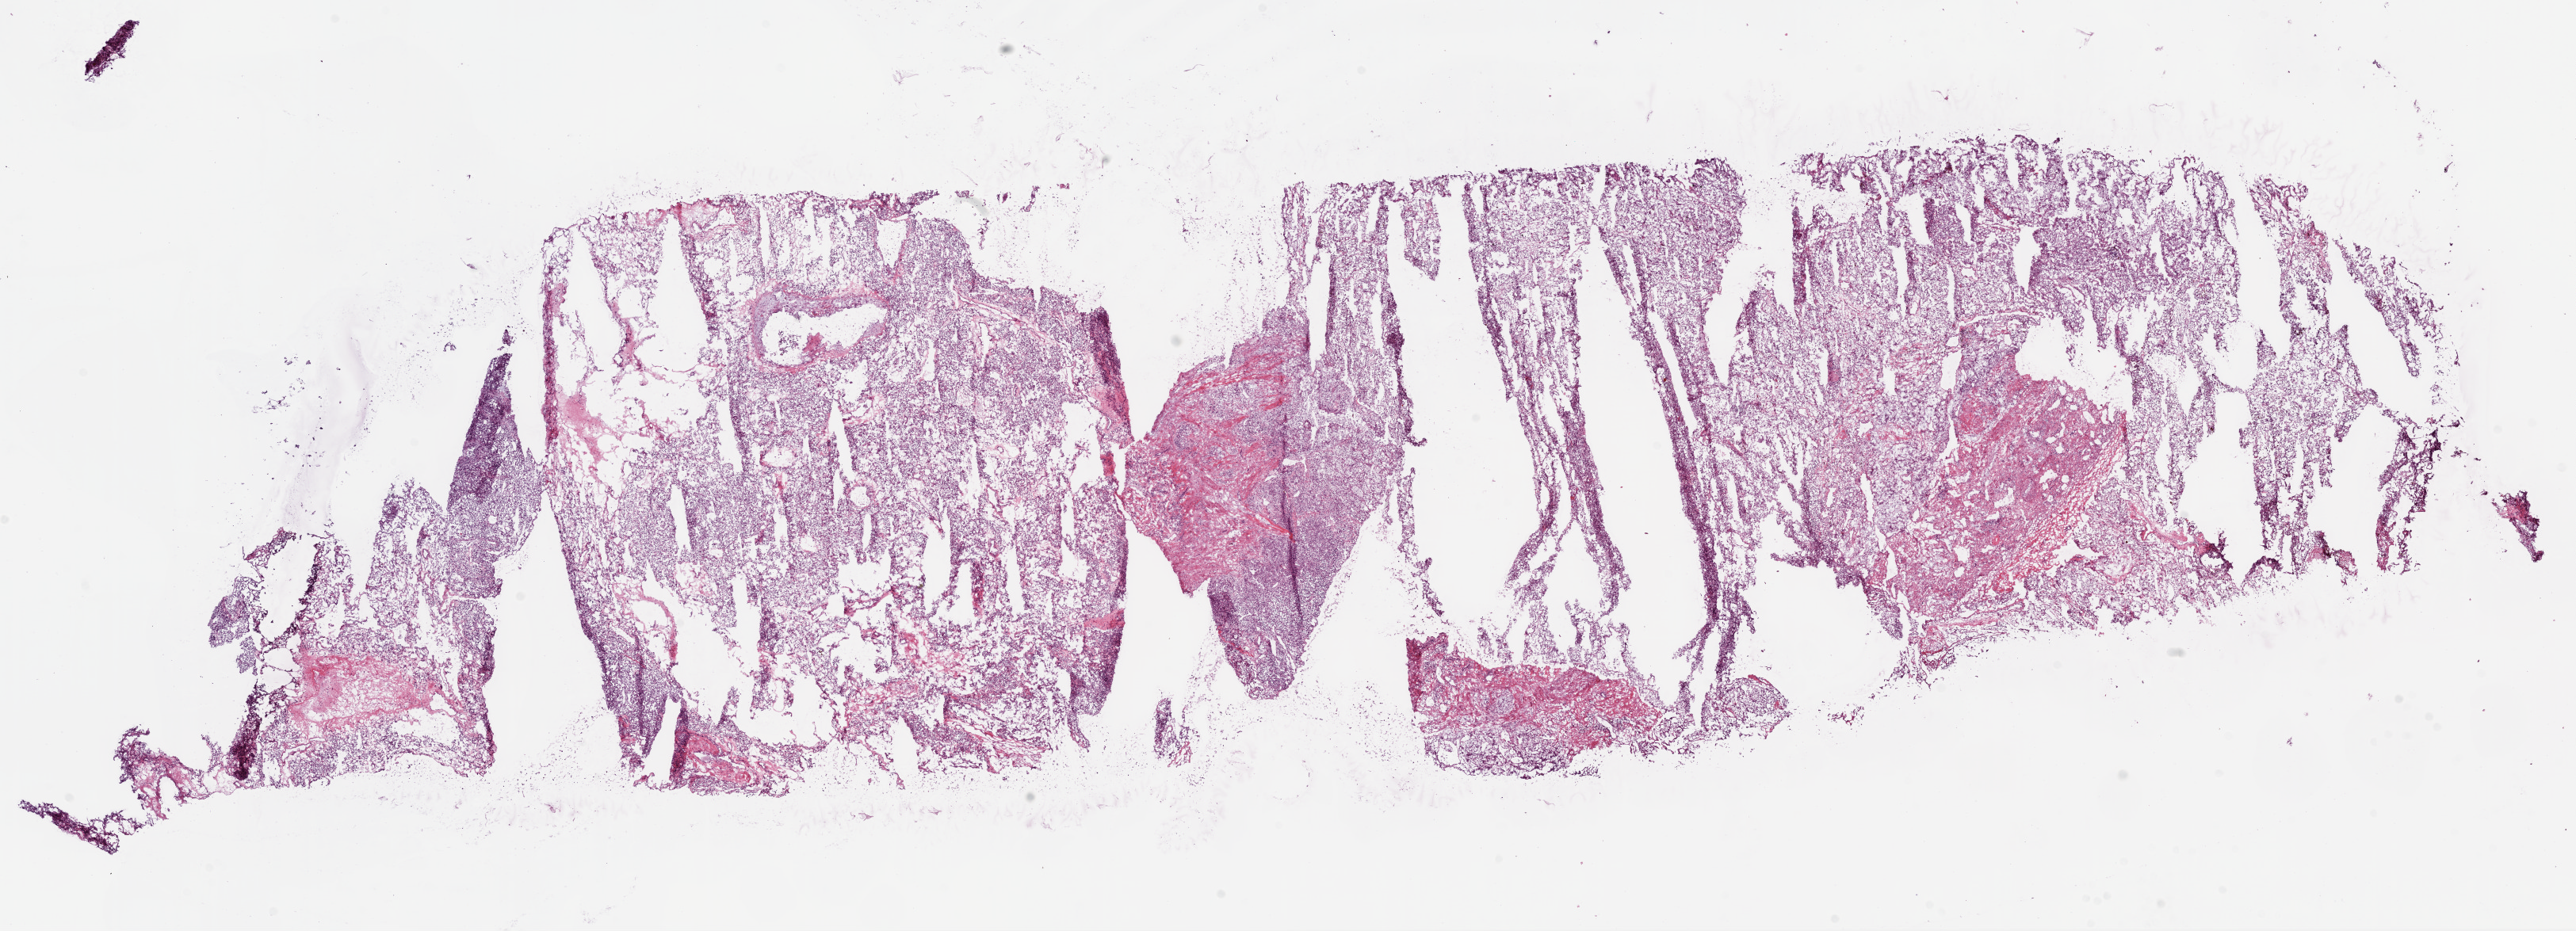
Digitized H&E tissue section (whole slide), low-resolution overview of the scanned area, about 26.1 x 9.4 mm (slide scanned at 20x). Frozen section. Sample: primary tumour, kidney. Patient: male, age at initial diagnosis 38 years.
Diagnosis: Clear cell adenocarcinoma, NOS.